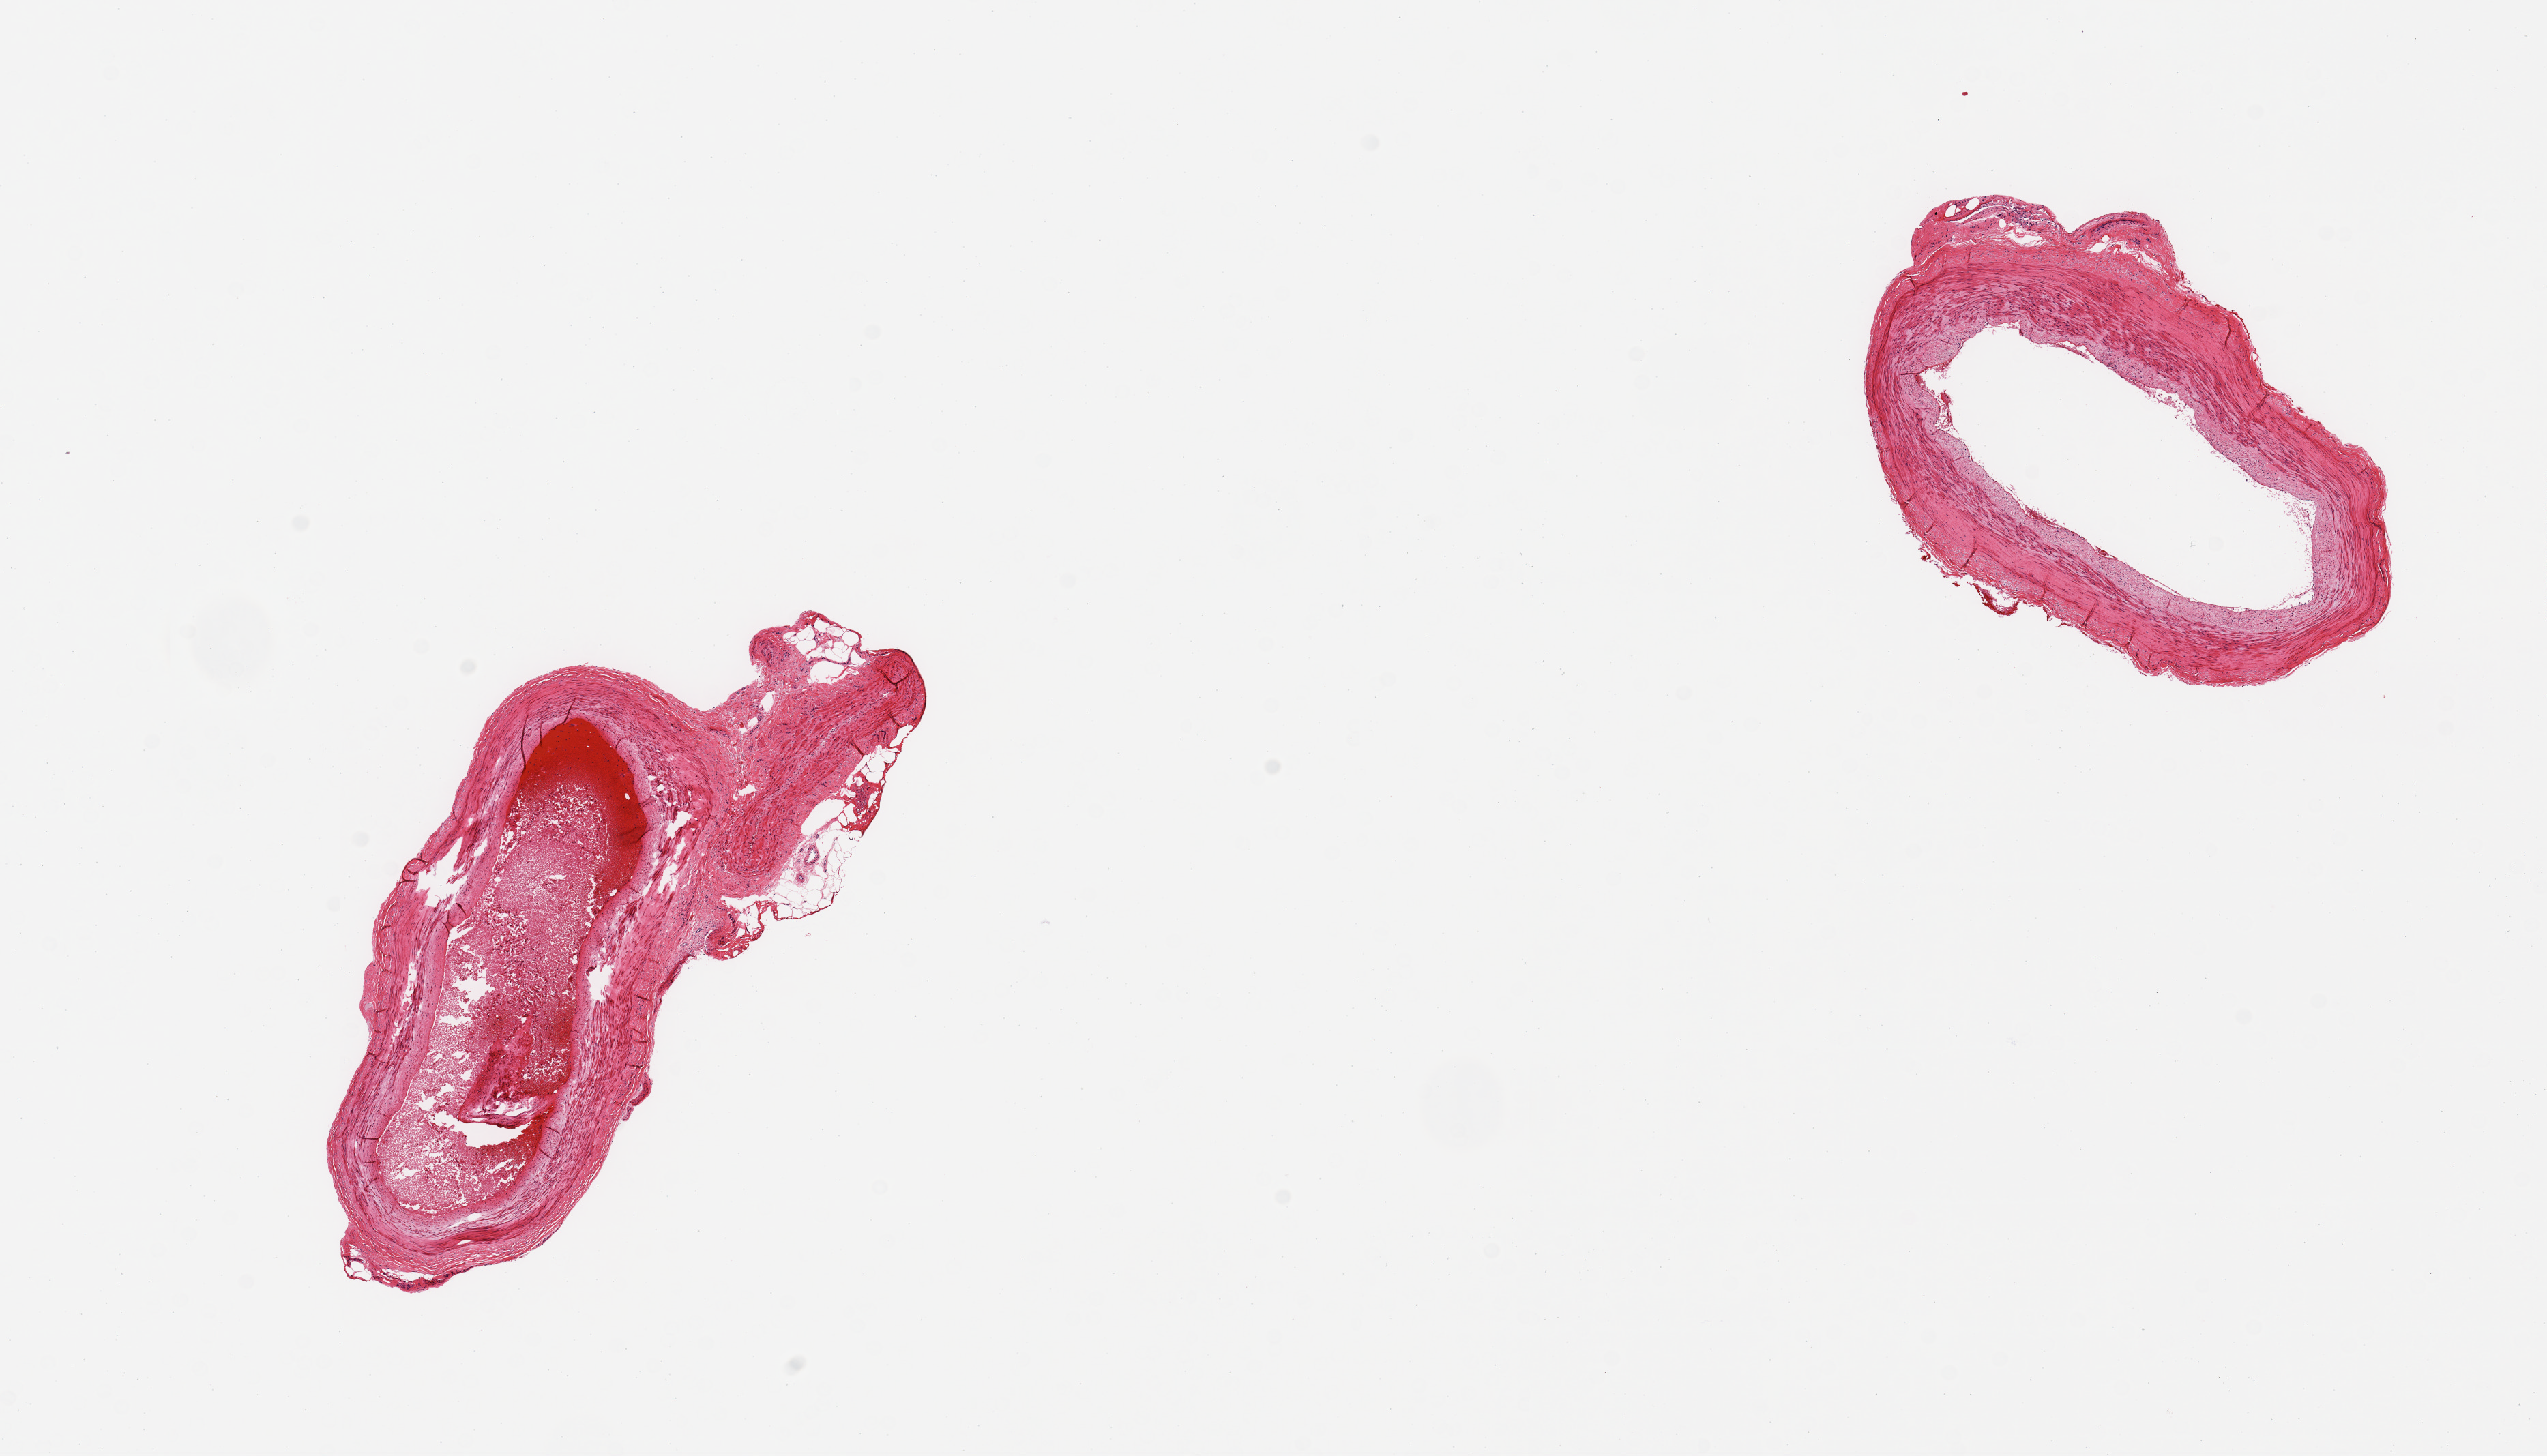
Whole-slide image, hematoxylin and eosin (H&E) stain — a low-resolution overview of the entire scanned area, about 14.8 x 8.4 mm (slide scanned at 20x). PAXgene-fixed paraffin-embedded (PFPE) section. Sampled site (target tissue): tibial artery. Tissue donor sample.
• review note (as recorded): 2 pieces; one includes attached portion of vein/fat; mild, focal plaque